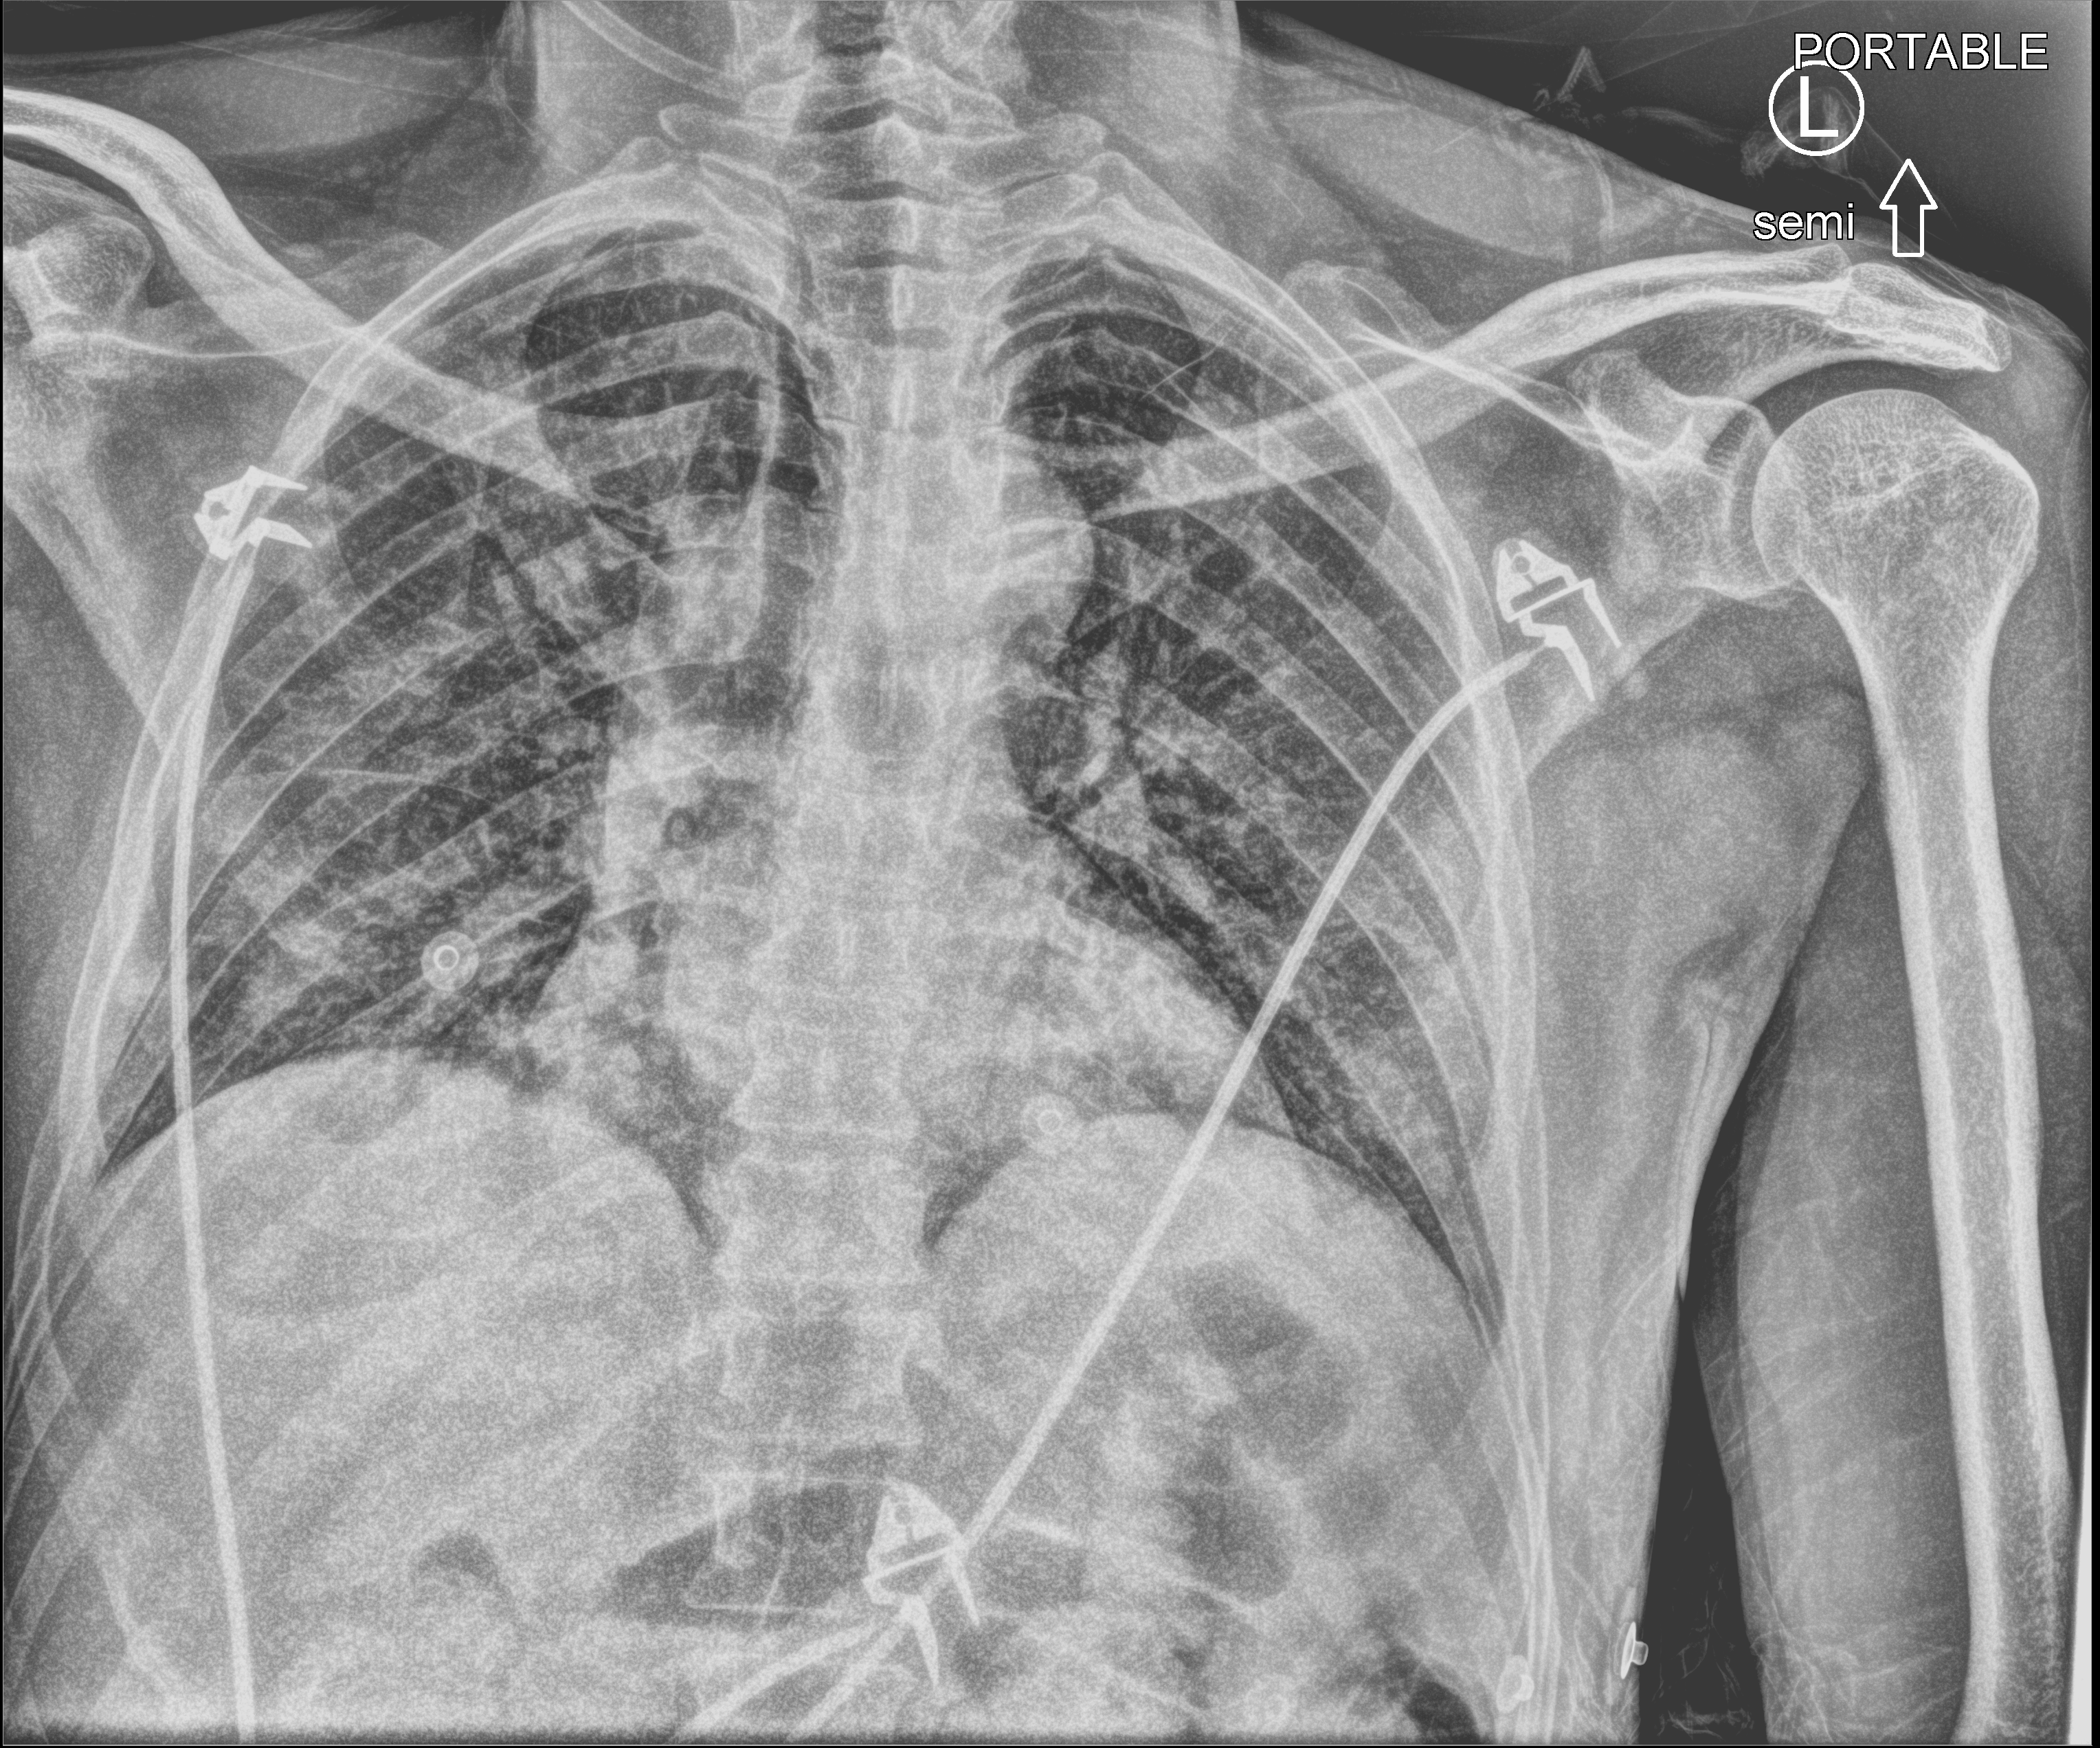
Chest X-ray (portable), anteroposterior (AP) projection. Male patient hospitalised with COVID-19, age 18–59 years.
Admission-level facts for this patient (not findings on this image; timing relative to this image not recorded): admitted to intensive care during this hospital stay: yes.